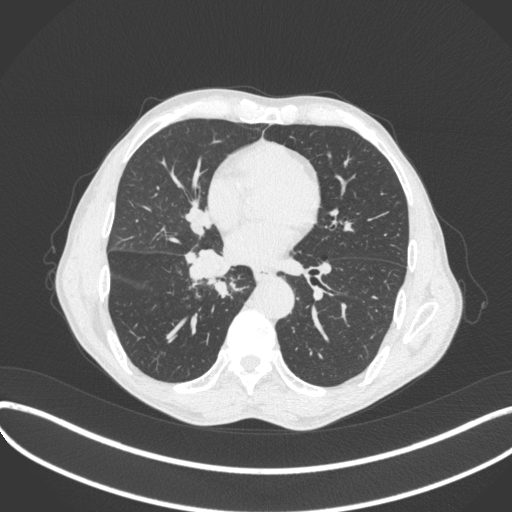
Chest CT, one axial slice. Slice 198 of 481 in the series (ordered by position). Reconstruction kernel B31f. 120 kVp. Lung window (W 1500 / L -600 HU). 1 mm slice thickness. 512 × 512 image matrix, field of view 400 × 400 mm. Male patient, age 65 years. Case-level facts recorded for this patient, not image findings: clinical TNM (as recorded): T2a N0 M0; histopathological grade: G2.
Structures marked on this image (bounding box drawn by a radiologist):
- lung tumour (recorded histology: squamous cell carcinoma): bounding box [x1, y1, x2, y2] px = [179, 246, 236, 281]